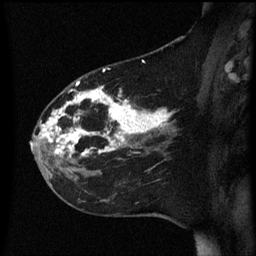
Breast MRI (dynamic contrast-enhanced), one sagittal slice; dynamic contrast-enhanced series, image 2 of 3 at this slice position (ordered by acquisition); 1.5 T; TE 4.2 ms, TR 8.4 ms; 2.2 mm slice thickness; 256 × 256 image matrix, field of view 200 × 200 mm. Patient: female, 35 years. Case-level facts recorded for this patient, not image findings: setting: breast cancer imaged before/during neoadjuvant chemotherapy; receptor status: HER2-positive.
Outlined on this slice (semi-automatic segmentation, software-assisted and operator-edited):
- analysis volume of interest (the breast-tissue region the enhancement analysis was run in; not a lesion): bounding box (x1, y1, x2, y2) in pixels: (32, 78, 173, 163)
- tumour enhancement mask (voxels above the 70 % enhancement threshold inside the analysis volume of interest): (32, 82, 173, 157)